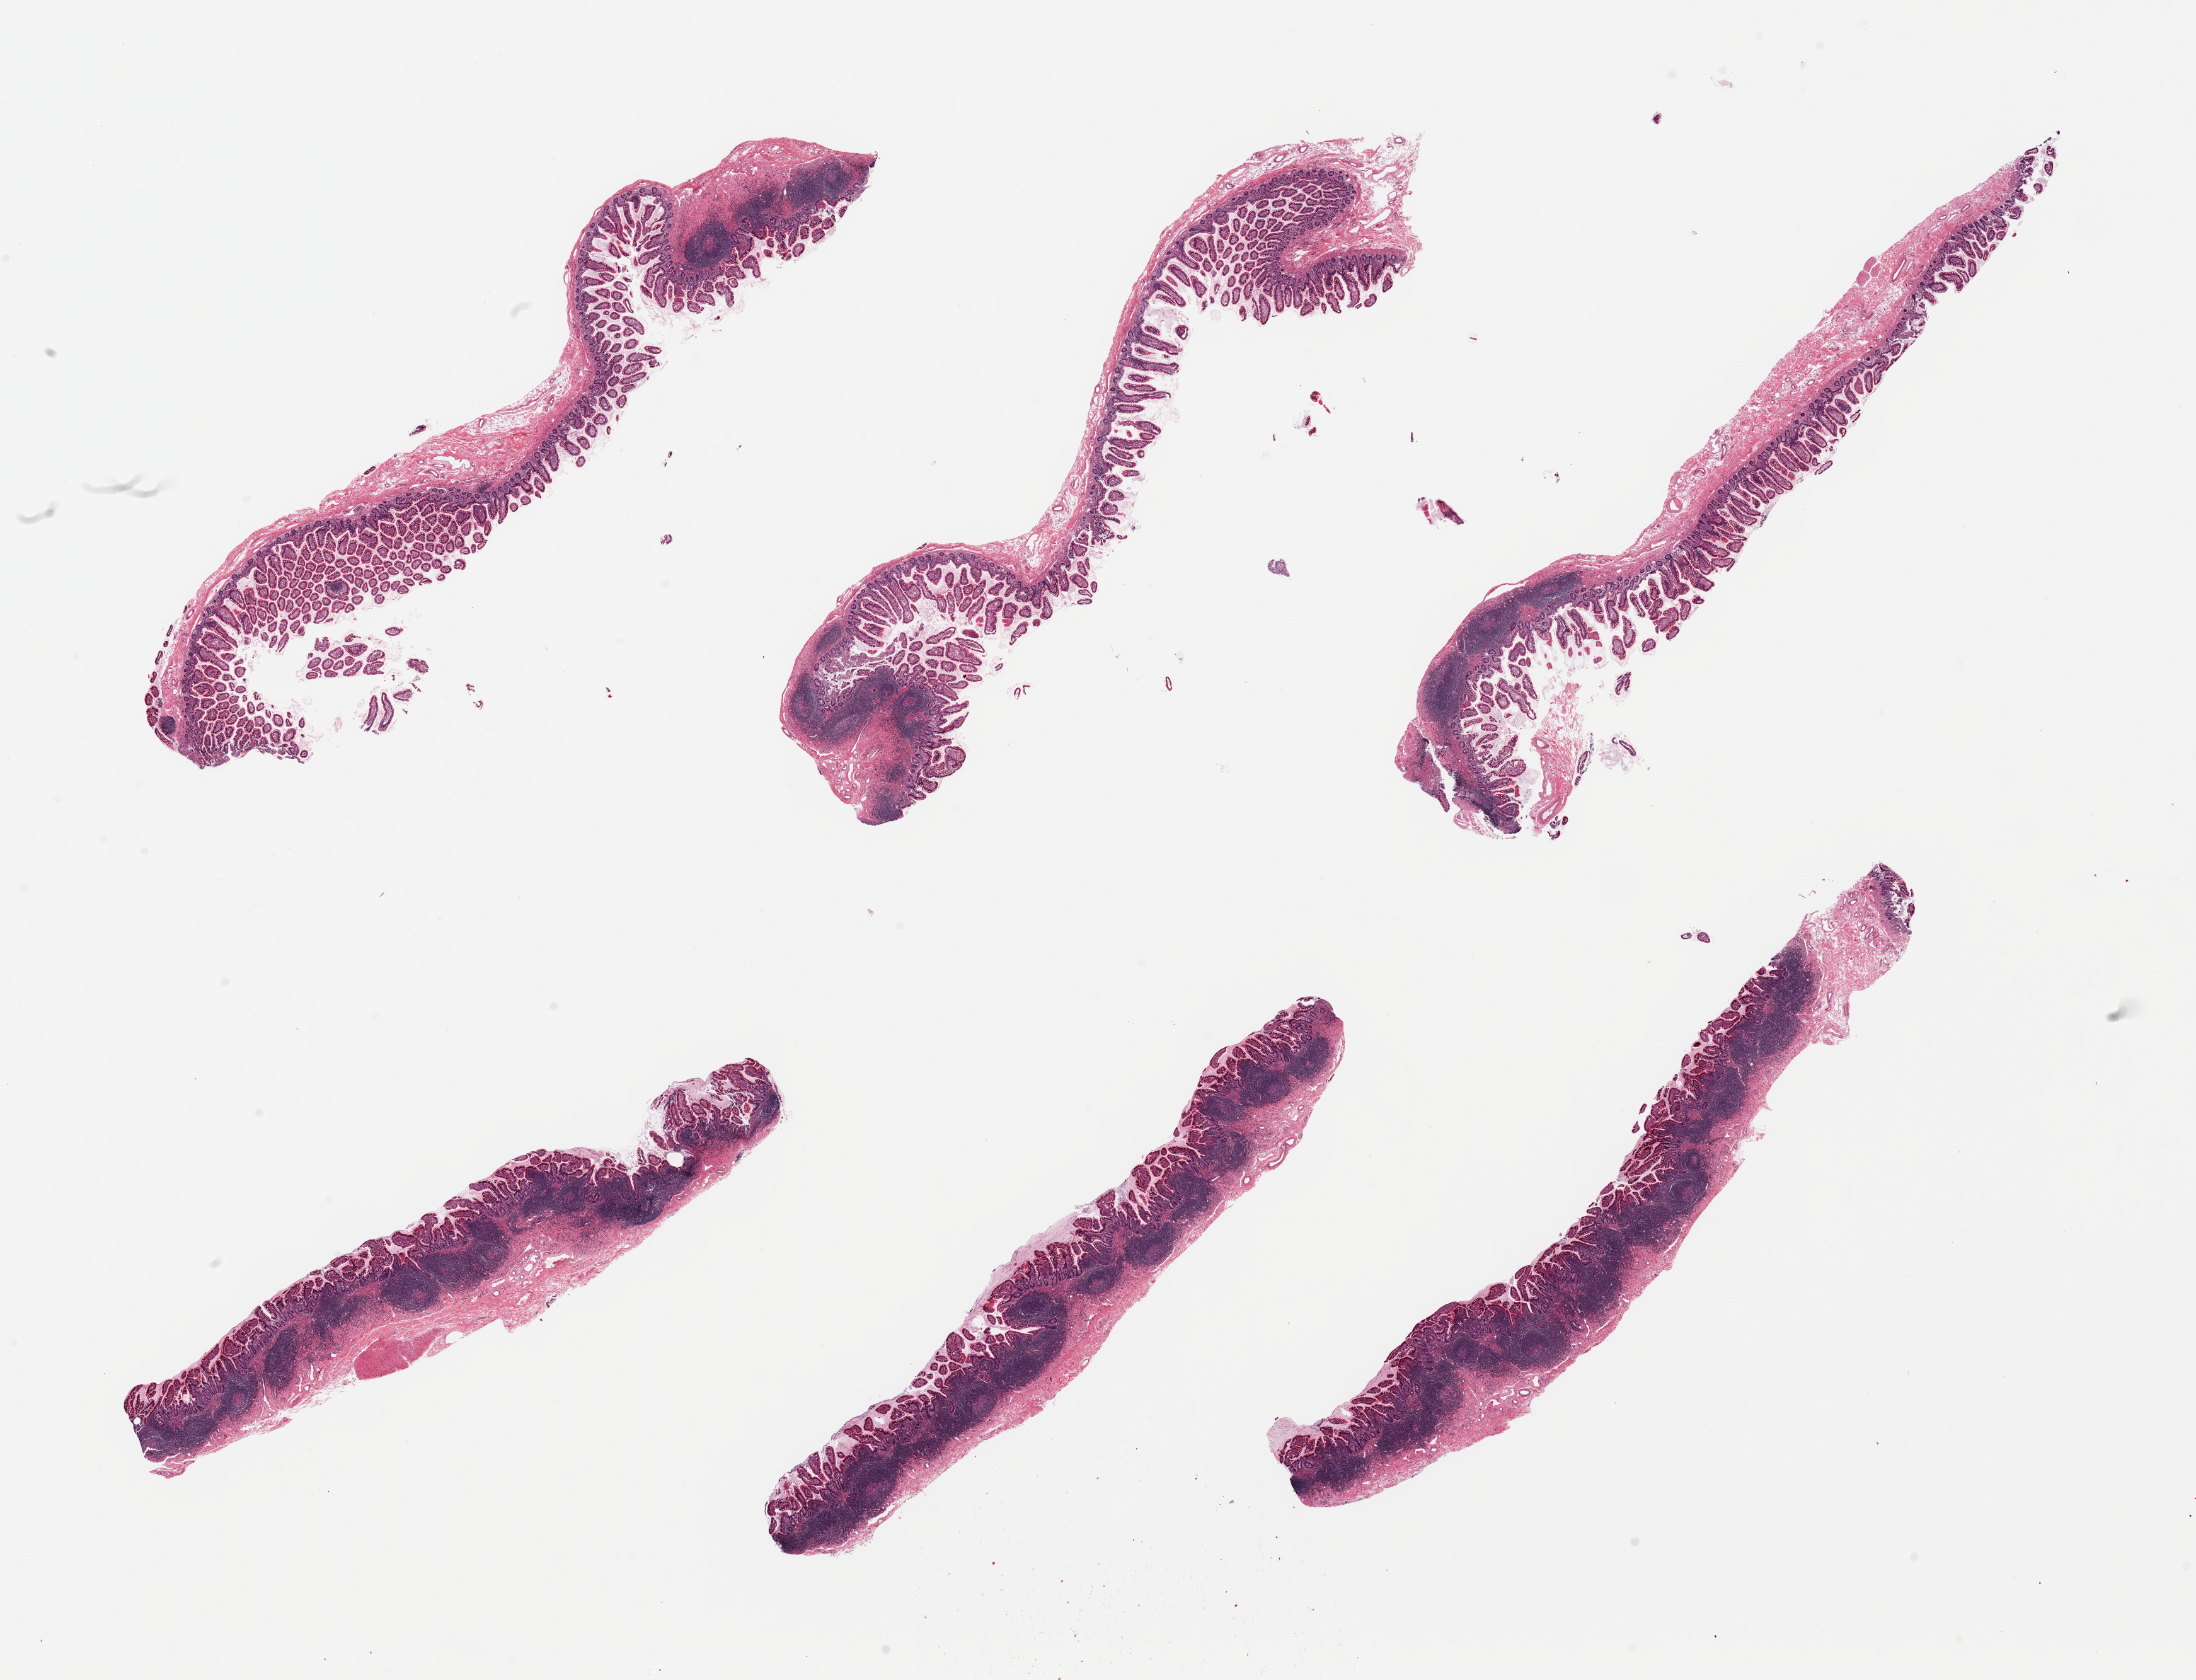
Whole-slide image, haematoxylin and eosin stain — whole scanned area (about 27.6 x 21.1 mm, slide scanned at 20x) shown as a low-resolution overview; PAXgene-fixed paraffin-embedded (PFPE) section; target tissue: ileum; tissue donor sample. Donor: female.
Reviewer comment on this tissue sample: 6 pieces, ~well preserved, lymphoid/Peyer aggregates are up to ~40% total tissue.